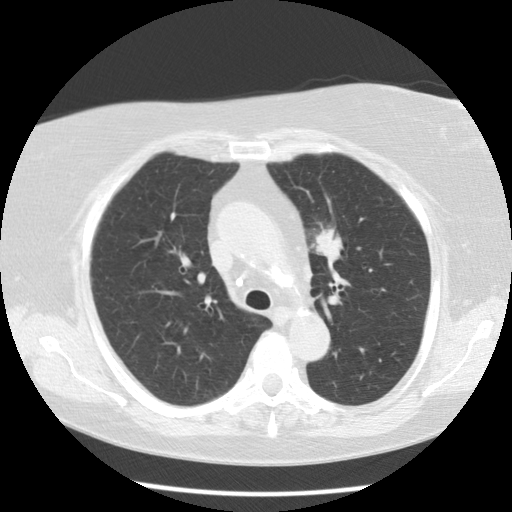
Axial slice from a low-dose chest CT screening exam, second annual screen, lung window (W 1500 / L -600 HU), 2.5 mm slice thickness, standard (soft-tissue) reconstruction kernel (STANDARD), slice 30 of 109 in the series. Female, age 67 years at enrolment. Former smoker at enrolment.
Lesion marked by an expert reader, bounding box [x1, y1, x2, y2] px = [292, 212, 352, 269]. The exam's reader record, not a measurement of the box and not confirmed to be the same lesion: non-calcified nodule or mass ≥4 mm, left upper lobe, 20 × 18 mm, poorly defined margins, soft tissue attenuation, pre-existing on the prior screen: yes; interval growth: yes.